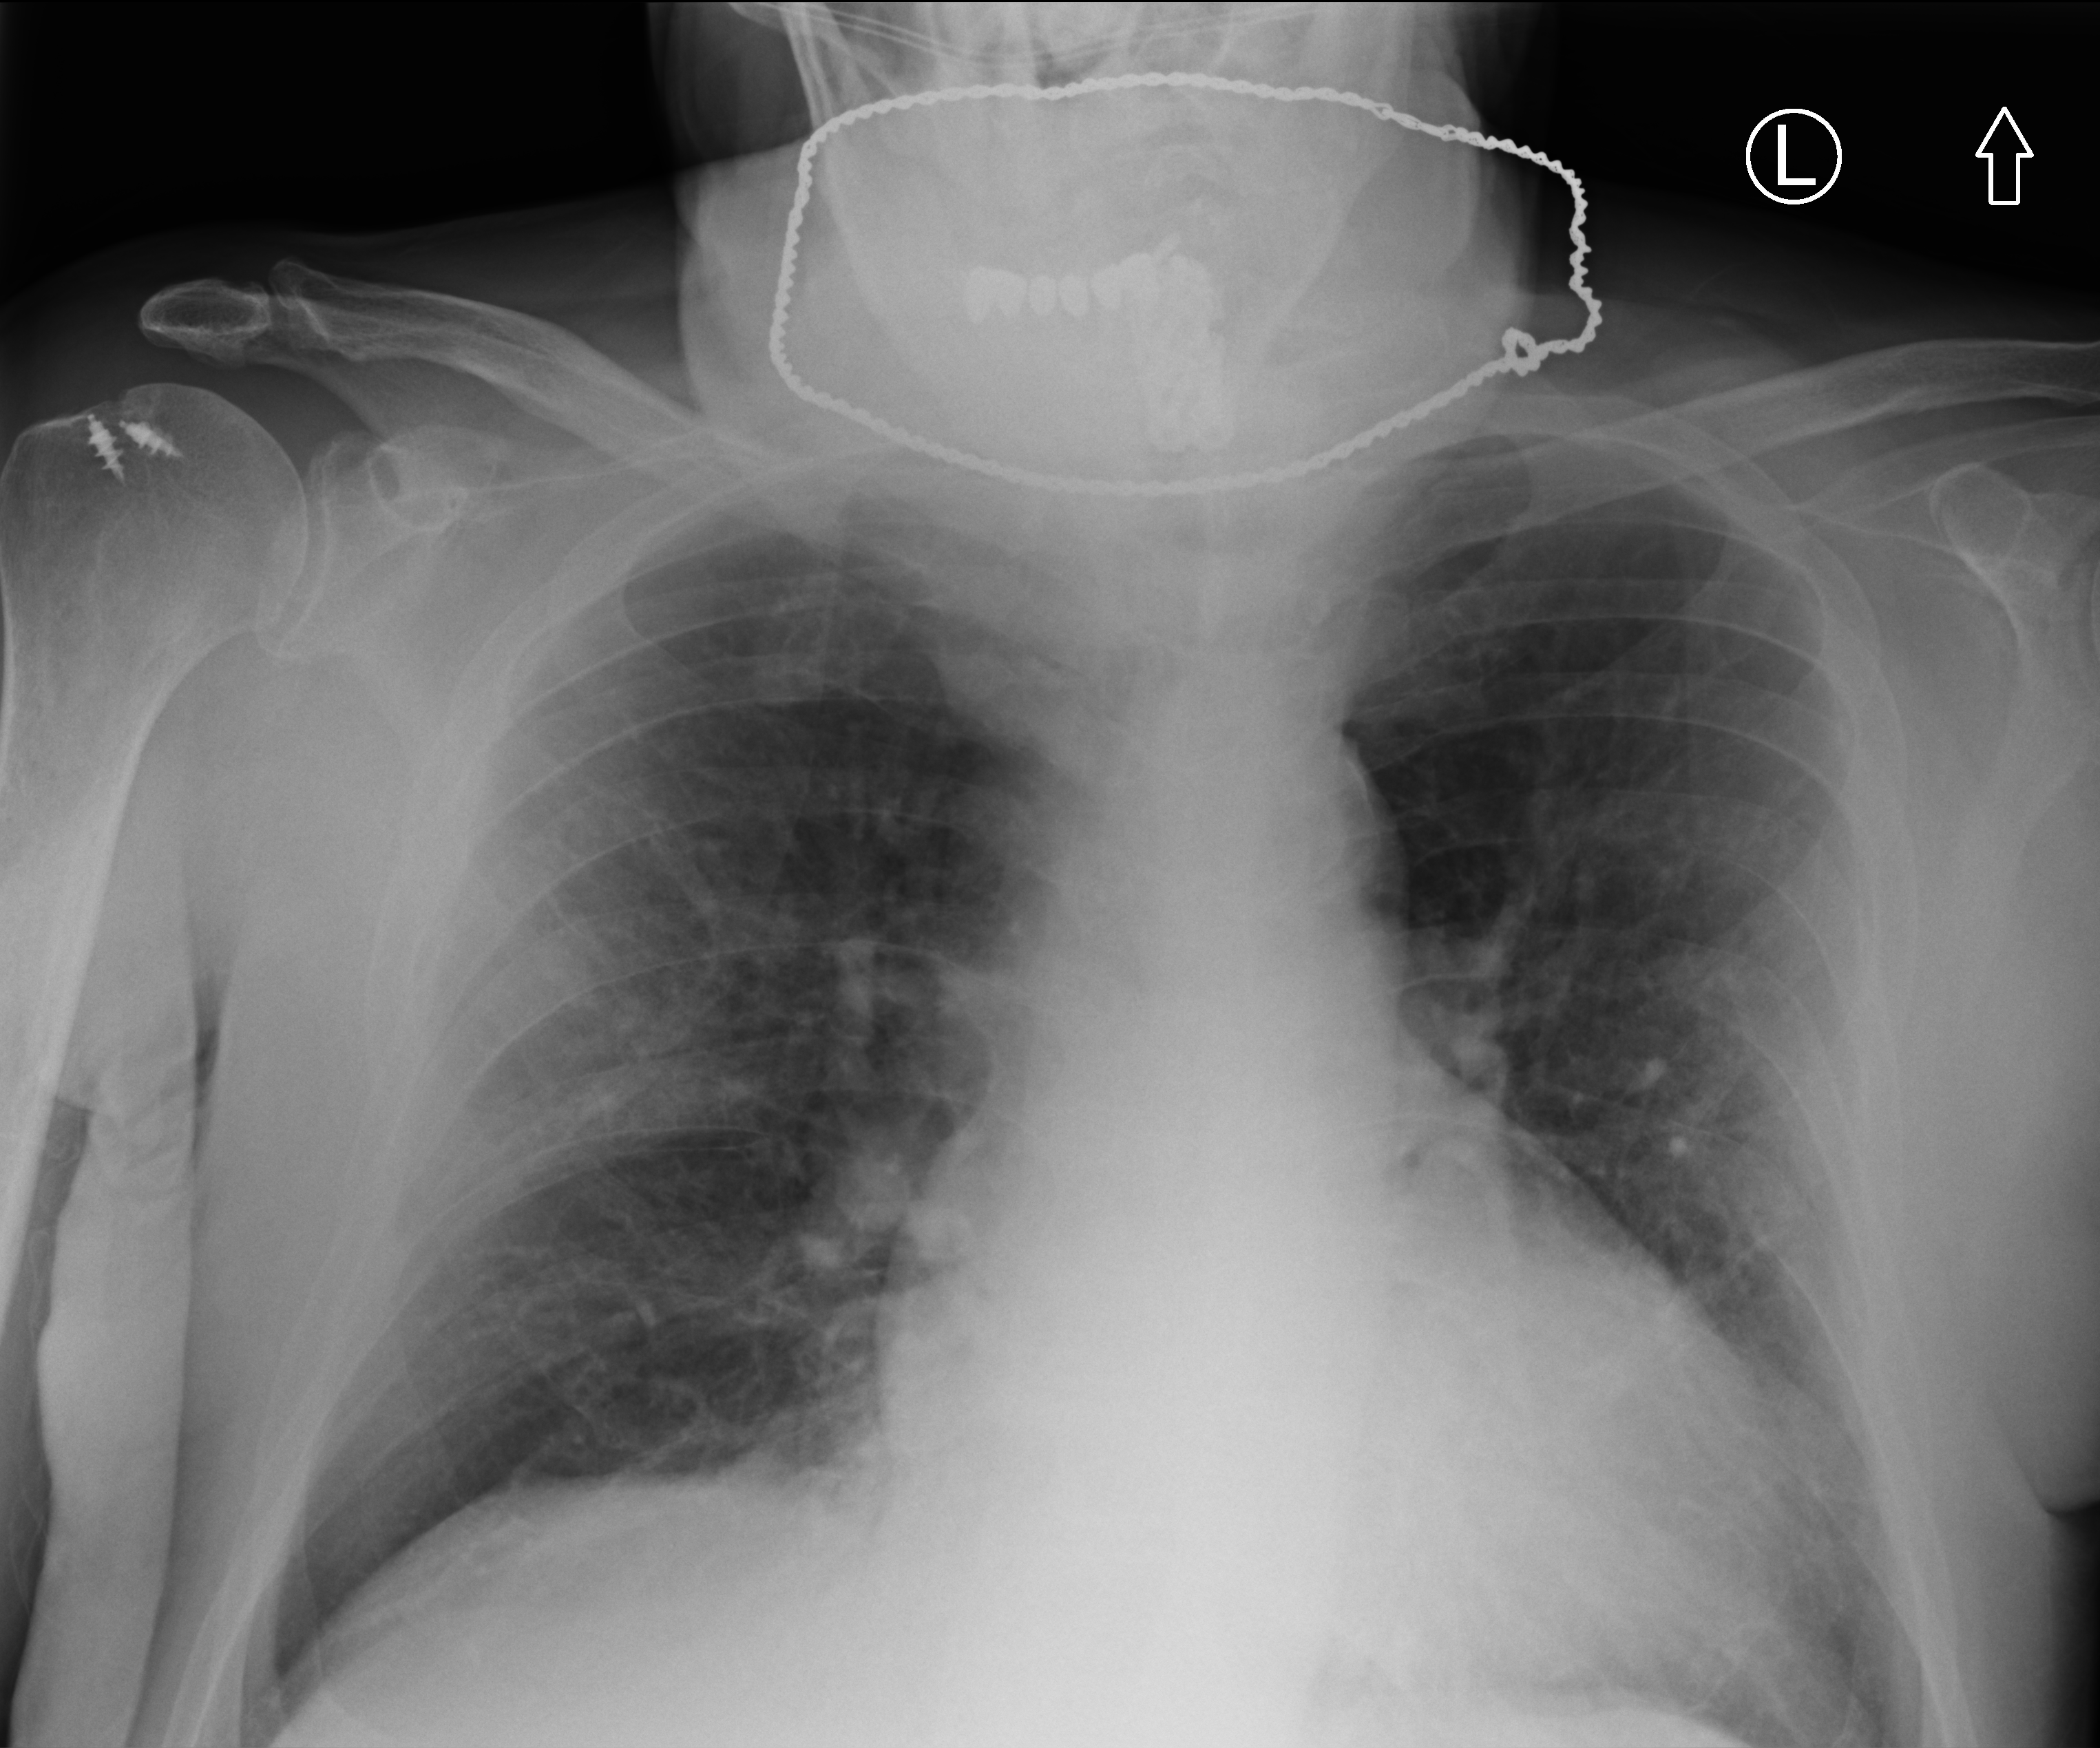
Bedside chest radiograph (computed radiography), anteroposterior (AP) projection. Patient hospitalised with COVID-19; male, aged 75–90 years.
From the hospital-stay record, not from the radiograph (when in the stay this image was taken is not recorded): mechanically ventilated during this hospital stay: yes.